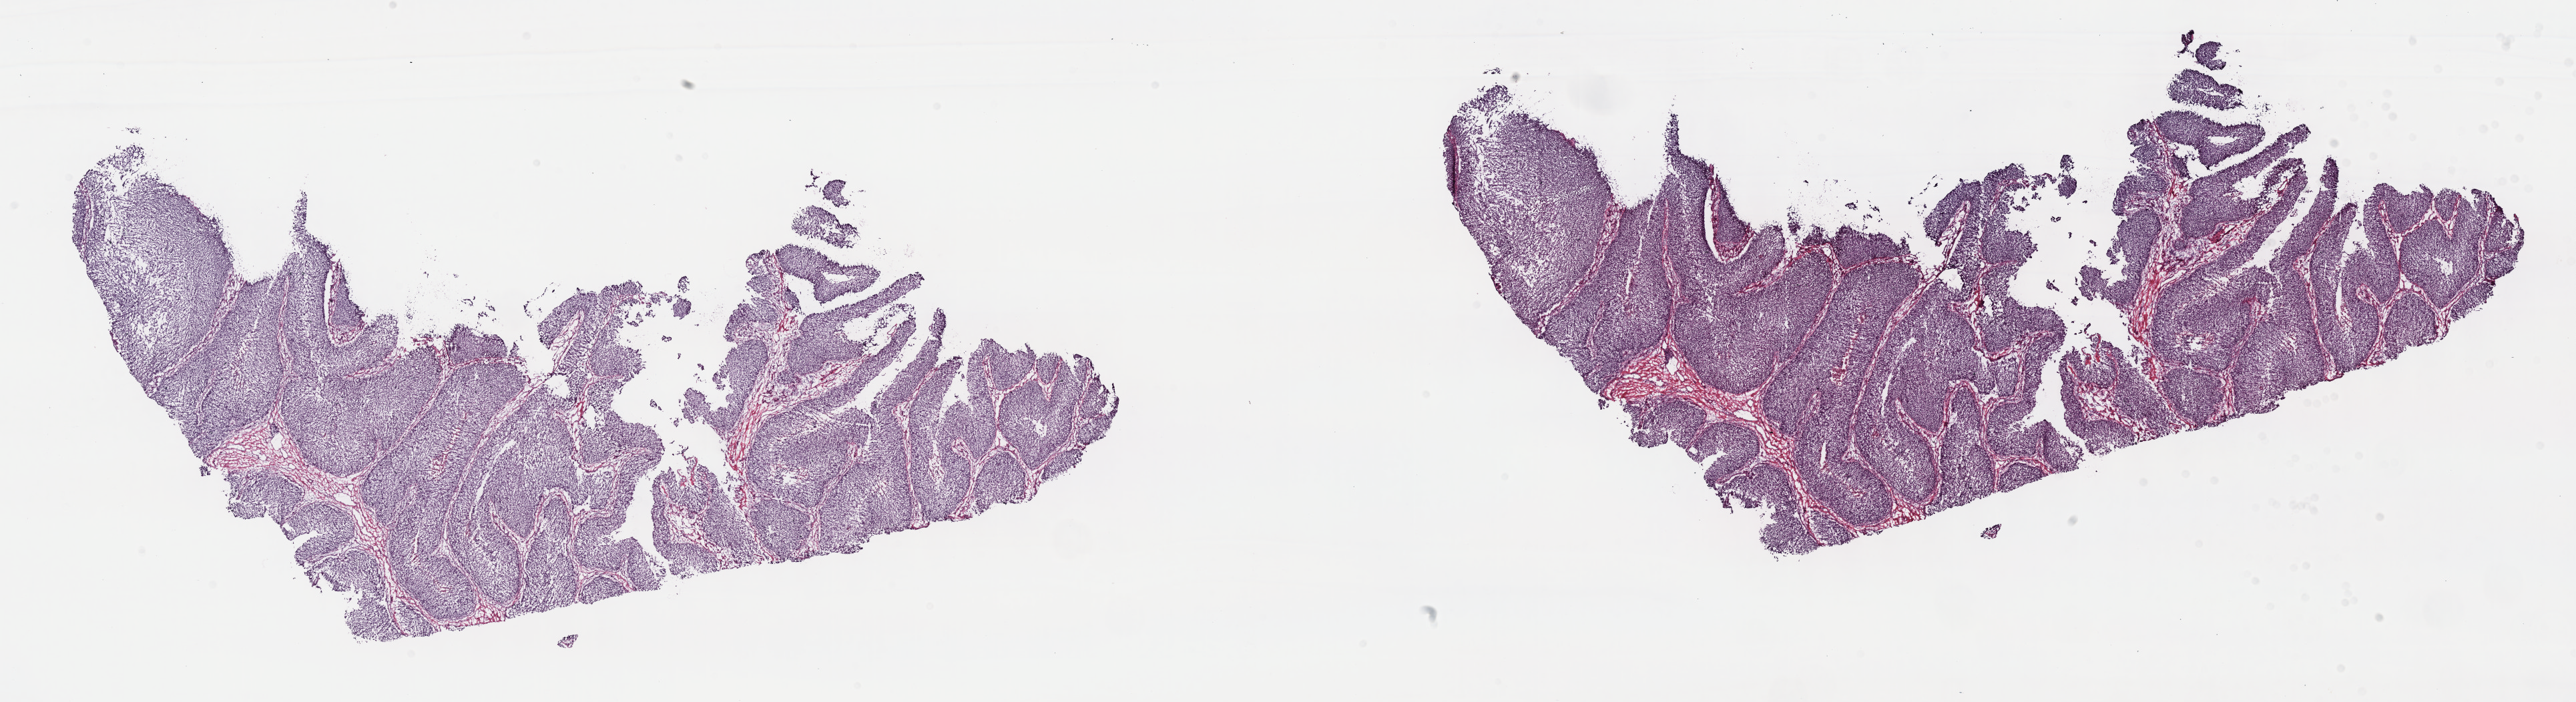
Hematoxylin and eosin (H&E) stained whole-slide image, shown as a low-resolution overview of the whole scanned area (about 31.2 x 8.5 mm, acquisition: 40x scan). Frozen section from the top of the tissue portion. Sample: primary tumour, bladder. Female, age 75 years at initial diagnosis. Histologic grade: high grade. Composition of this section per pathologist review: tumour cells 78%, tumour nuclei 90%, normal cells 0%, stromal cells 18%, necrosis 4%. Inflammatory infiltration, as recorded: lymphocyte infiltration 7%, monocyte infiltration 0%, neutrophil infiltration 0%.
• AJCC pathologic stage: III
• TNM: T4a N0 M0
• pathologic diagnosis: Papillary transitional cell carcinoma
• lymph nodes positive (case pathology): 0 of 53 examined